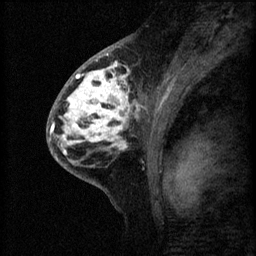
Breast MRI (dynamic contrast-enhanced), one sagittal slice. Slice 33 of 60 in the series (ordered by position). 3 images stored at this slice position (order not interpretable as contrast timing). 1.5 T. TE 4.2 ms, TR 8.2 ms. 2 mm slice thickness. 256 × 256 image matrix, field of view 180 × 180 mm. Patient: female, 41 years.
Outlined on this slice (semi-automatically segmented with operator editing):
- analysis volume of interest (the breast-tissue region the enhancement analysis was run in; not a lesion): bounding box <53,62,160,175> (left, top, right, bottom; pixels)
- tumour enhancement mask (voxels above the 70 % enhancement threshold inside the analysis volume of interest): <53,62,143,155>